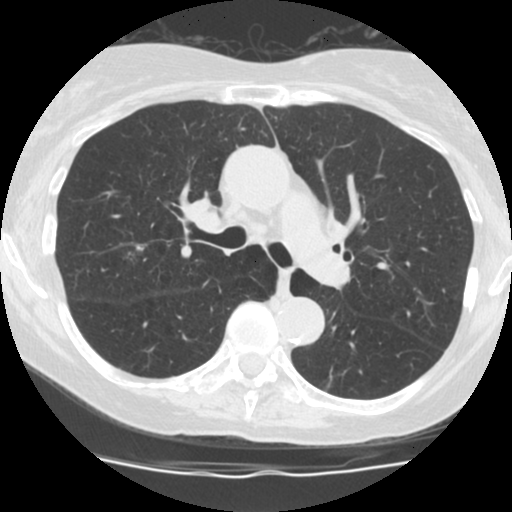
Low-dose screening chest CT, one axial slice; slice 117 of 183 in the series (ordered by position); reconstruction kernel STANDARD; lung window (W 1500 / L -600 HU); 2.5 mm slice thickness; 512 × 512 image matrix, field of view 300 × 300 mm.
Annotated regions visible in this slice (manually delineated by an expert):
- lesion 1 (tumor, upper lobe of right lung): bounding box <136,245,144,251> (left, top, right, bottom; pixels)